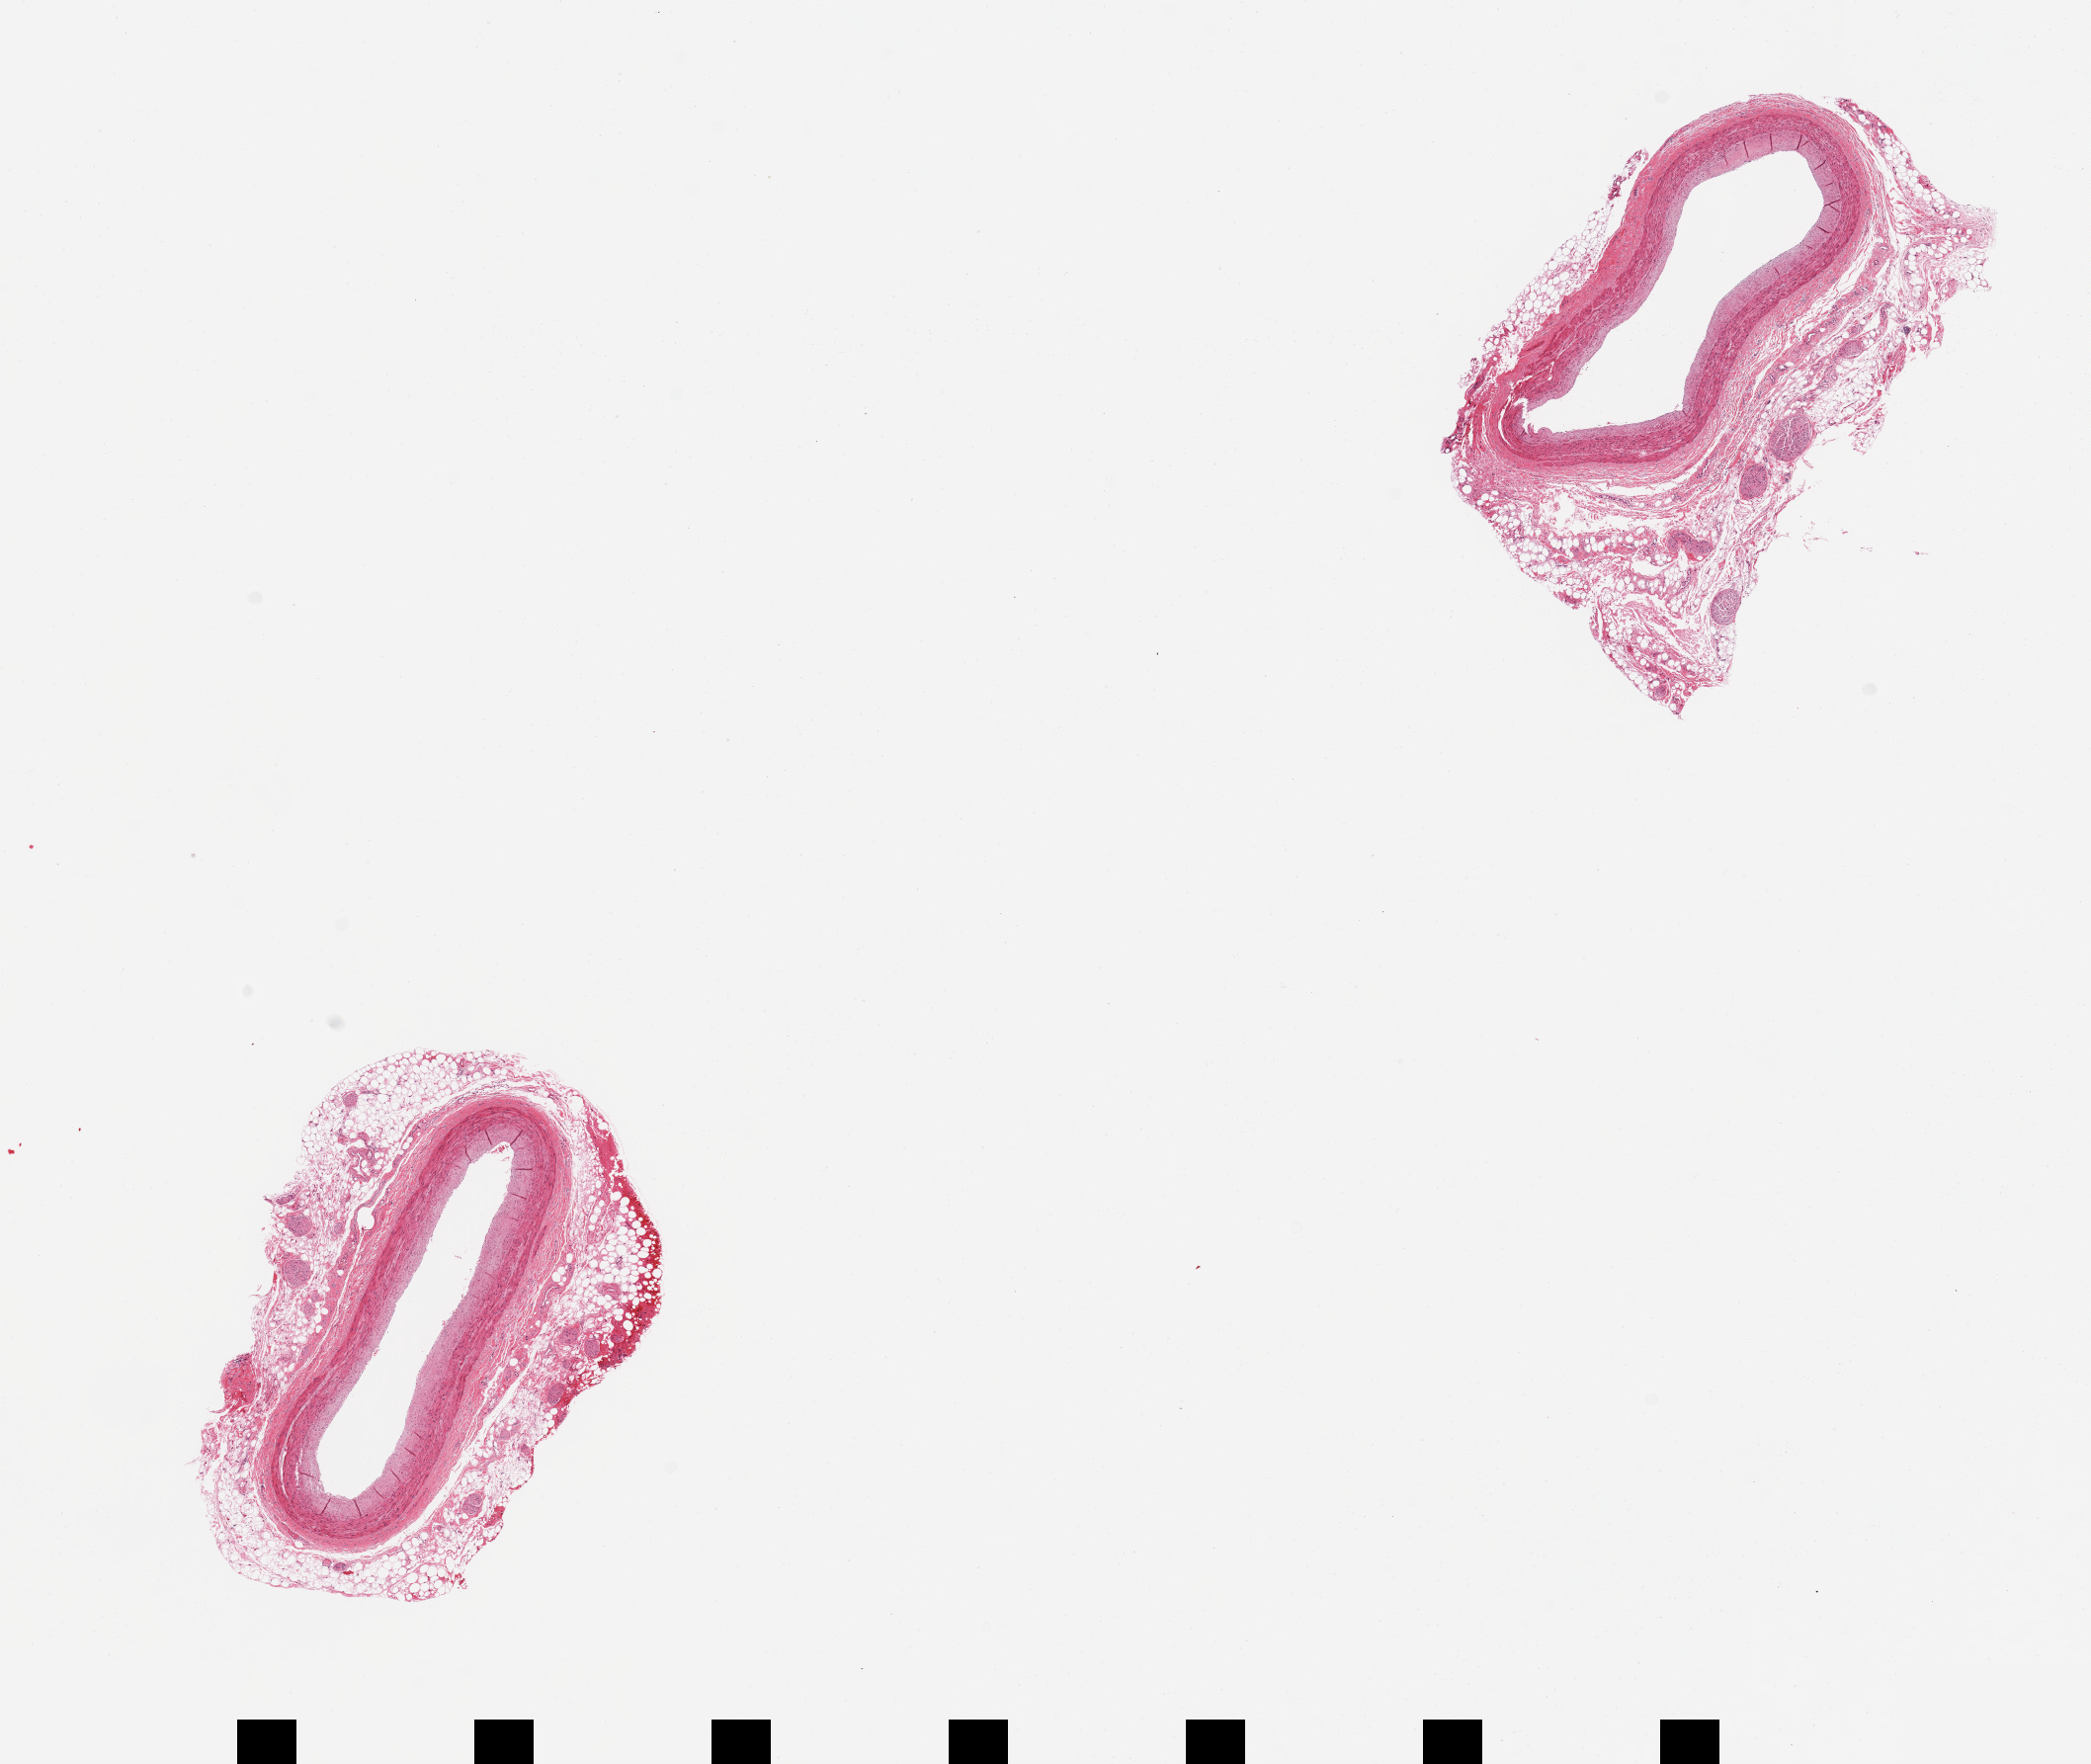
Whole-slide image, H&E stain, shown as a low-resolution overview of the whole scanned area (about 16.7 x 14.1 mm); PAXgene-fixed, paraffin-embedded tissue; target tissue: coronary artery; donor tissue sample. Female donor.
* pathologist's review note for this sample: 2 pieces, minimal atherosis; adherent rims of fat up to 1-2mm, deineated